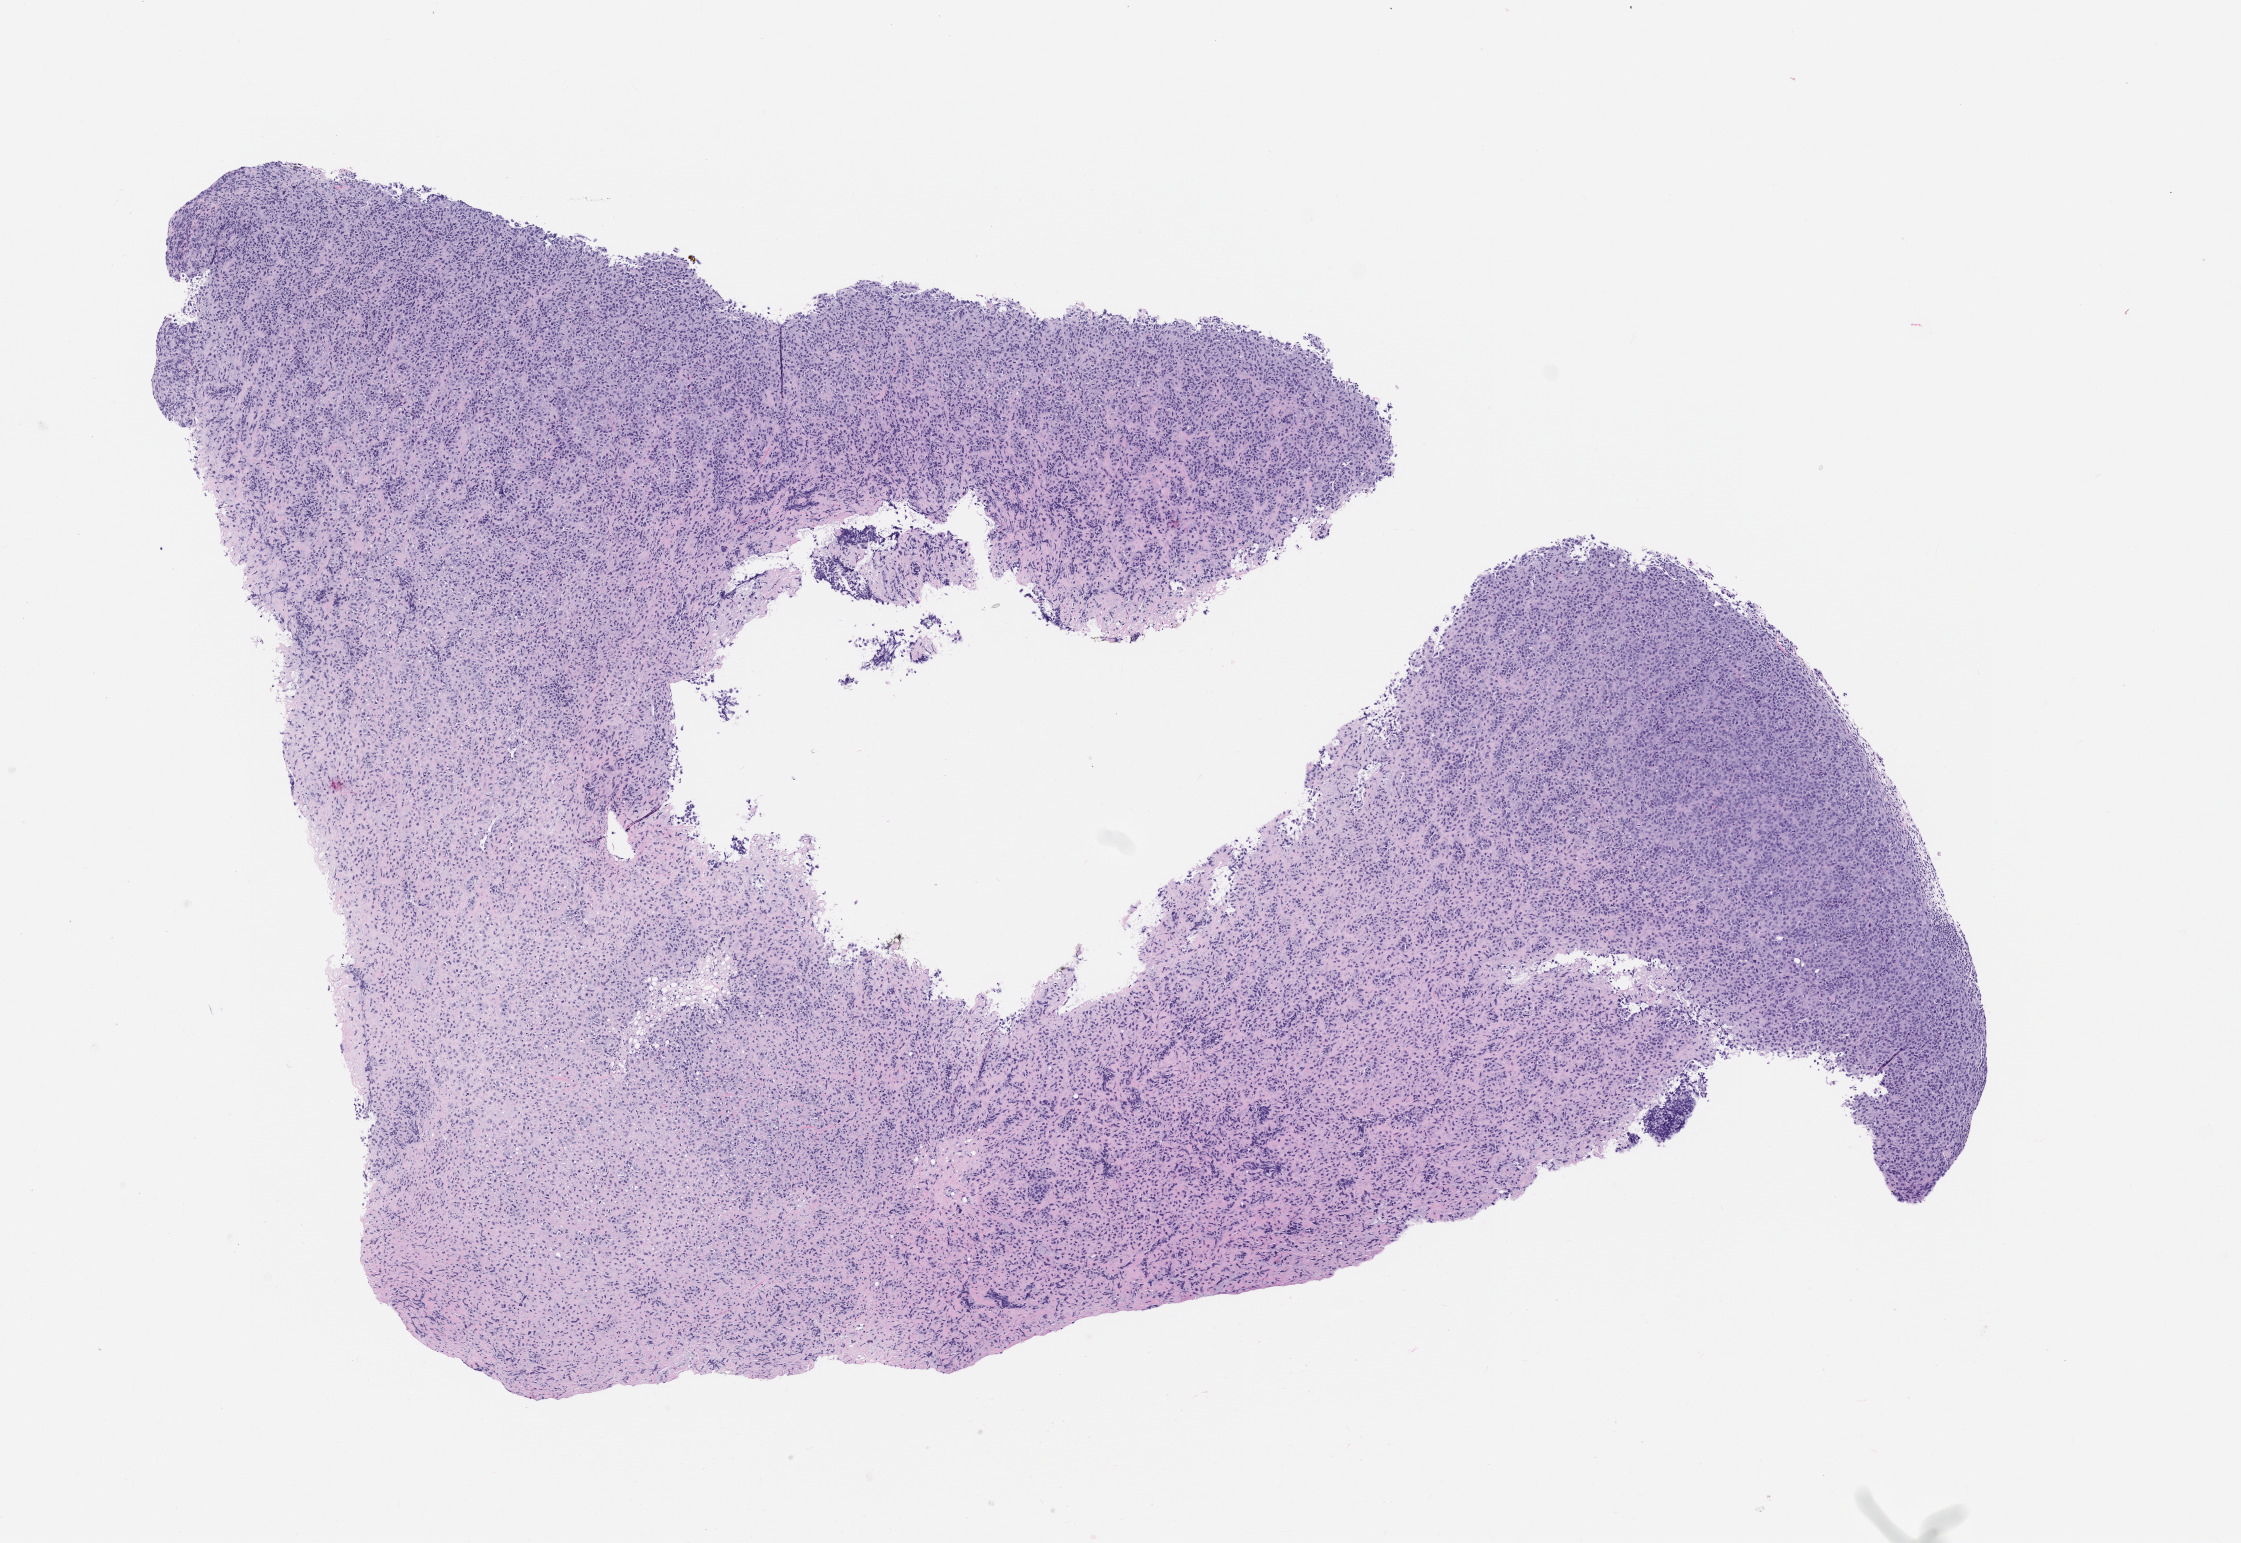
Whole-slide image, haematoxylin and eosin: patient-derived xenograft (human tumor grown in a mouse), passage 0 — a low-resolution overview of the entire scanned area, about 9.0 x 6.2 mm; FFPE section; tumor site category: bone.
Originating patient diagnosis: Osteosarcoma.